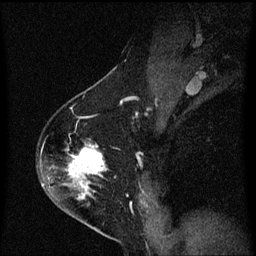
Breast MRI (dynamic contrast-enhanced), one sagittal slice. Position 41 of 60 along the scan axis. Dynamic contrast-enhanced series, image 2 of 3 at this slice position (ordered by acquisition). 1.5 T. TE 4.2 ms, TR 8.4 ms. 2 mm slice thickness. 256 × 256 image matrix, field of view 200 × 200 mm. Female patient, age 54 years. Case-level facts recorded for this patient, not image findings: setting: breast cancer imaged before/during neoadjuvant chemotherapy; receptor status: HER2-positive.
Structures marked on this image (semi-automatic segmentation, software-assisted and operator-edited):
- analysis volume of interest (the breast-tissue region the enhancement analysis was run in; not a lesion): bounding box (x1, y1, x2, y2) in pixels: (40, 144, 109, 213)
- tumour enhancement mask (voxels above the 70 % enhancement threshold inside the analysis volume of interest): (66, 148, 105, 197)